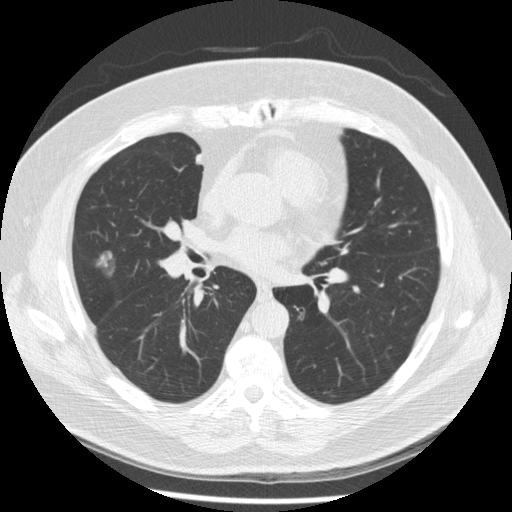
Low-dose screening chest CT, one axial slice. Slice 116 of 230 in the series (ordered by position). Lung window (W 1500 / L -600 HU). 2.5 mm slice thickness. 512 × 512 image matrix, field of view 360 × 360 mm.
Structures marked on this image (outlined manually by an expert reader):
- lesion 1 (tumor, middle lobe of right lung): bounding box <98,251,116,277> (left, top, right, bottom; pixels)